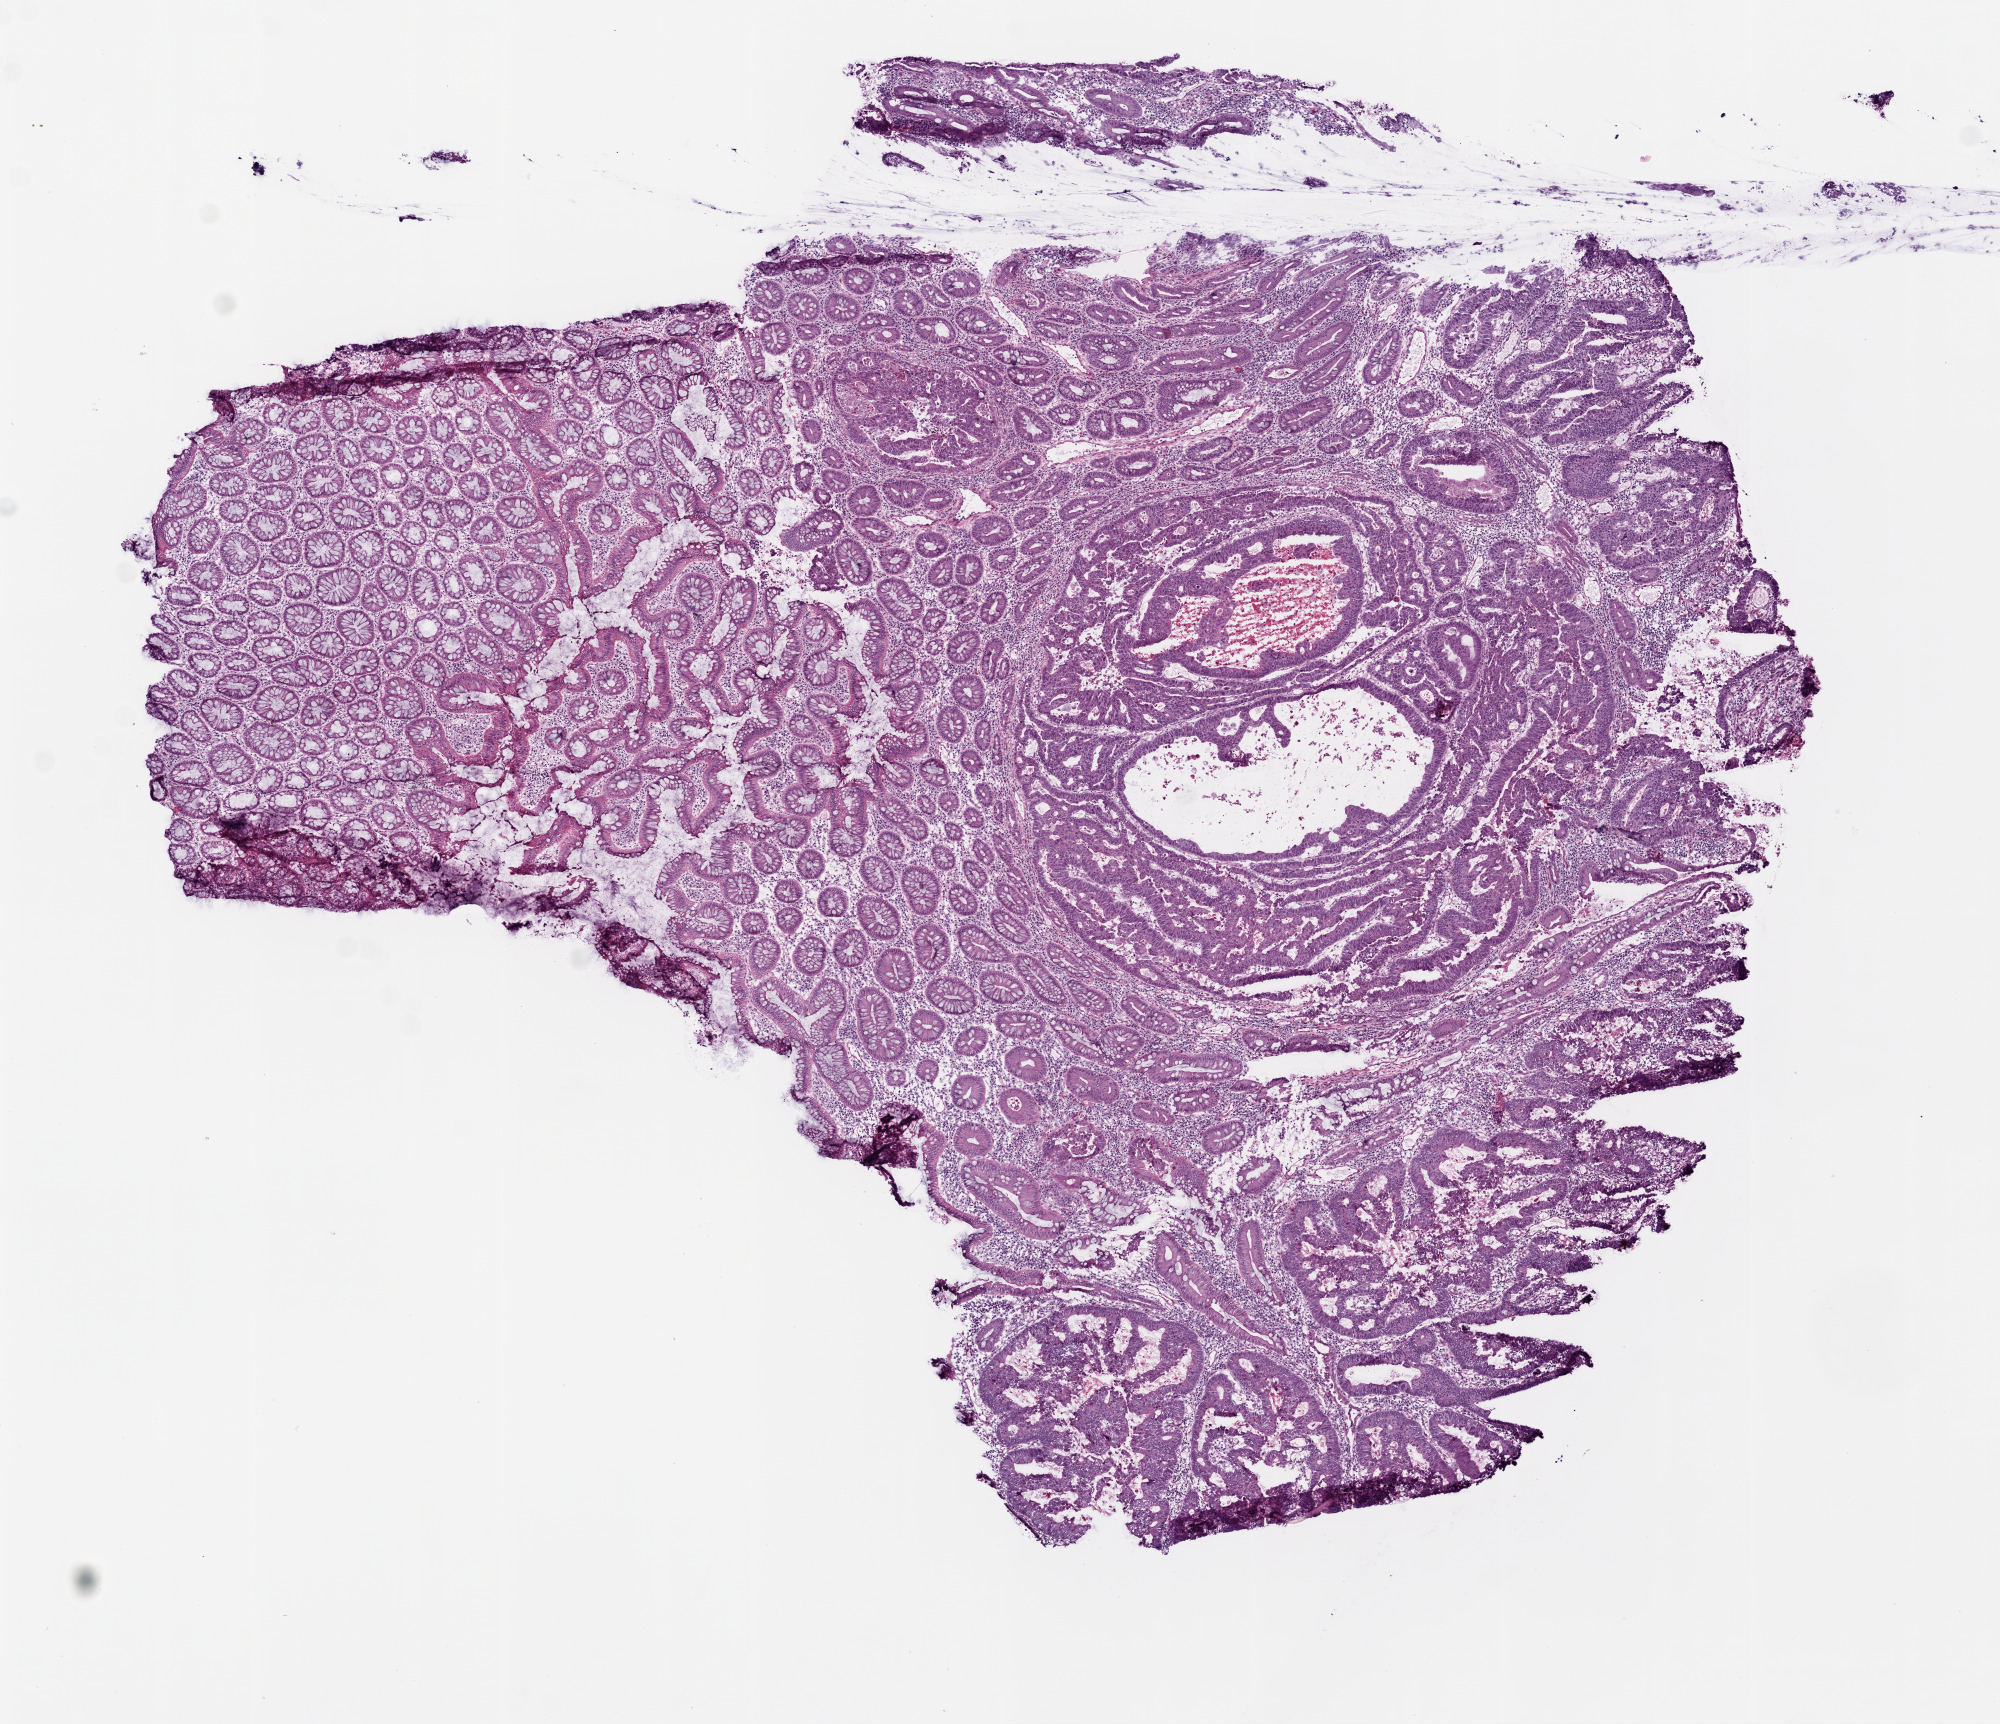
Hematoxylin and eosin (H&E) stained whole-slide image — shown as a low-resolution overview of the whole scanned area (about 8.0 x 6.9 mm). Frozen section from the top of the tissue portion. Sample: primary tumour, colon. Patient: male, age at initial diagnosis 64 years. Slide review estimates, as recorded: tumour cells 50%, tumour nuclei 50%, normal cells 50%, stromal cells 0%, necrosis 0%.
* lymph nodes positive (case pathology): 0 of 27 examined
* AJCC pathologic stage: IIA (6th edition)
* histologic diagnosis: Adenocarcinoma, NOS (descending colon)